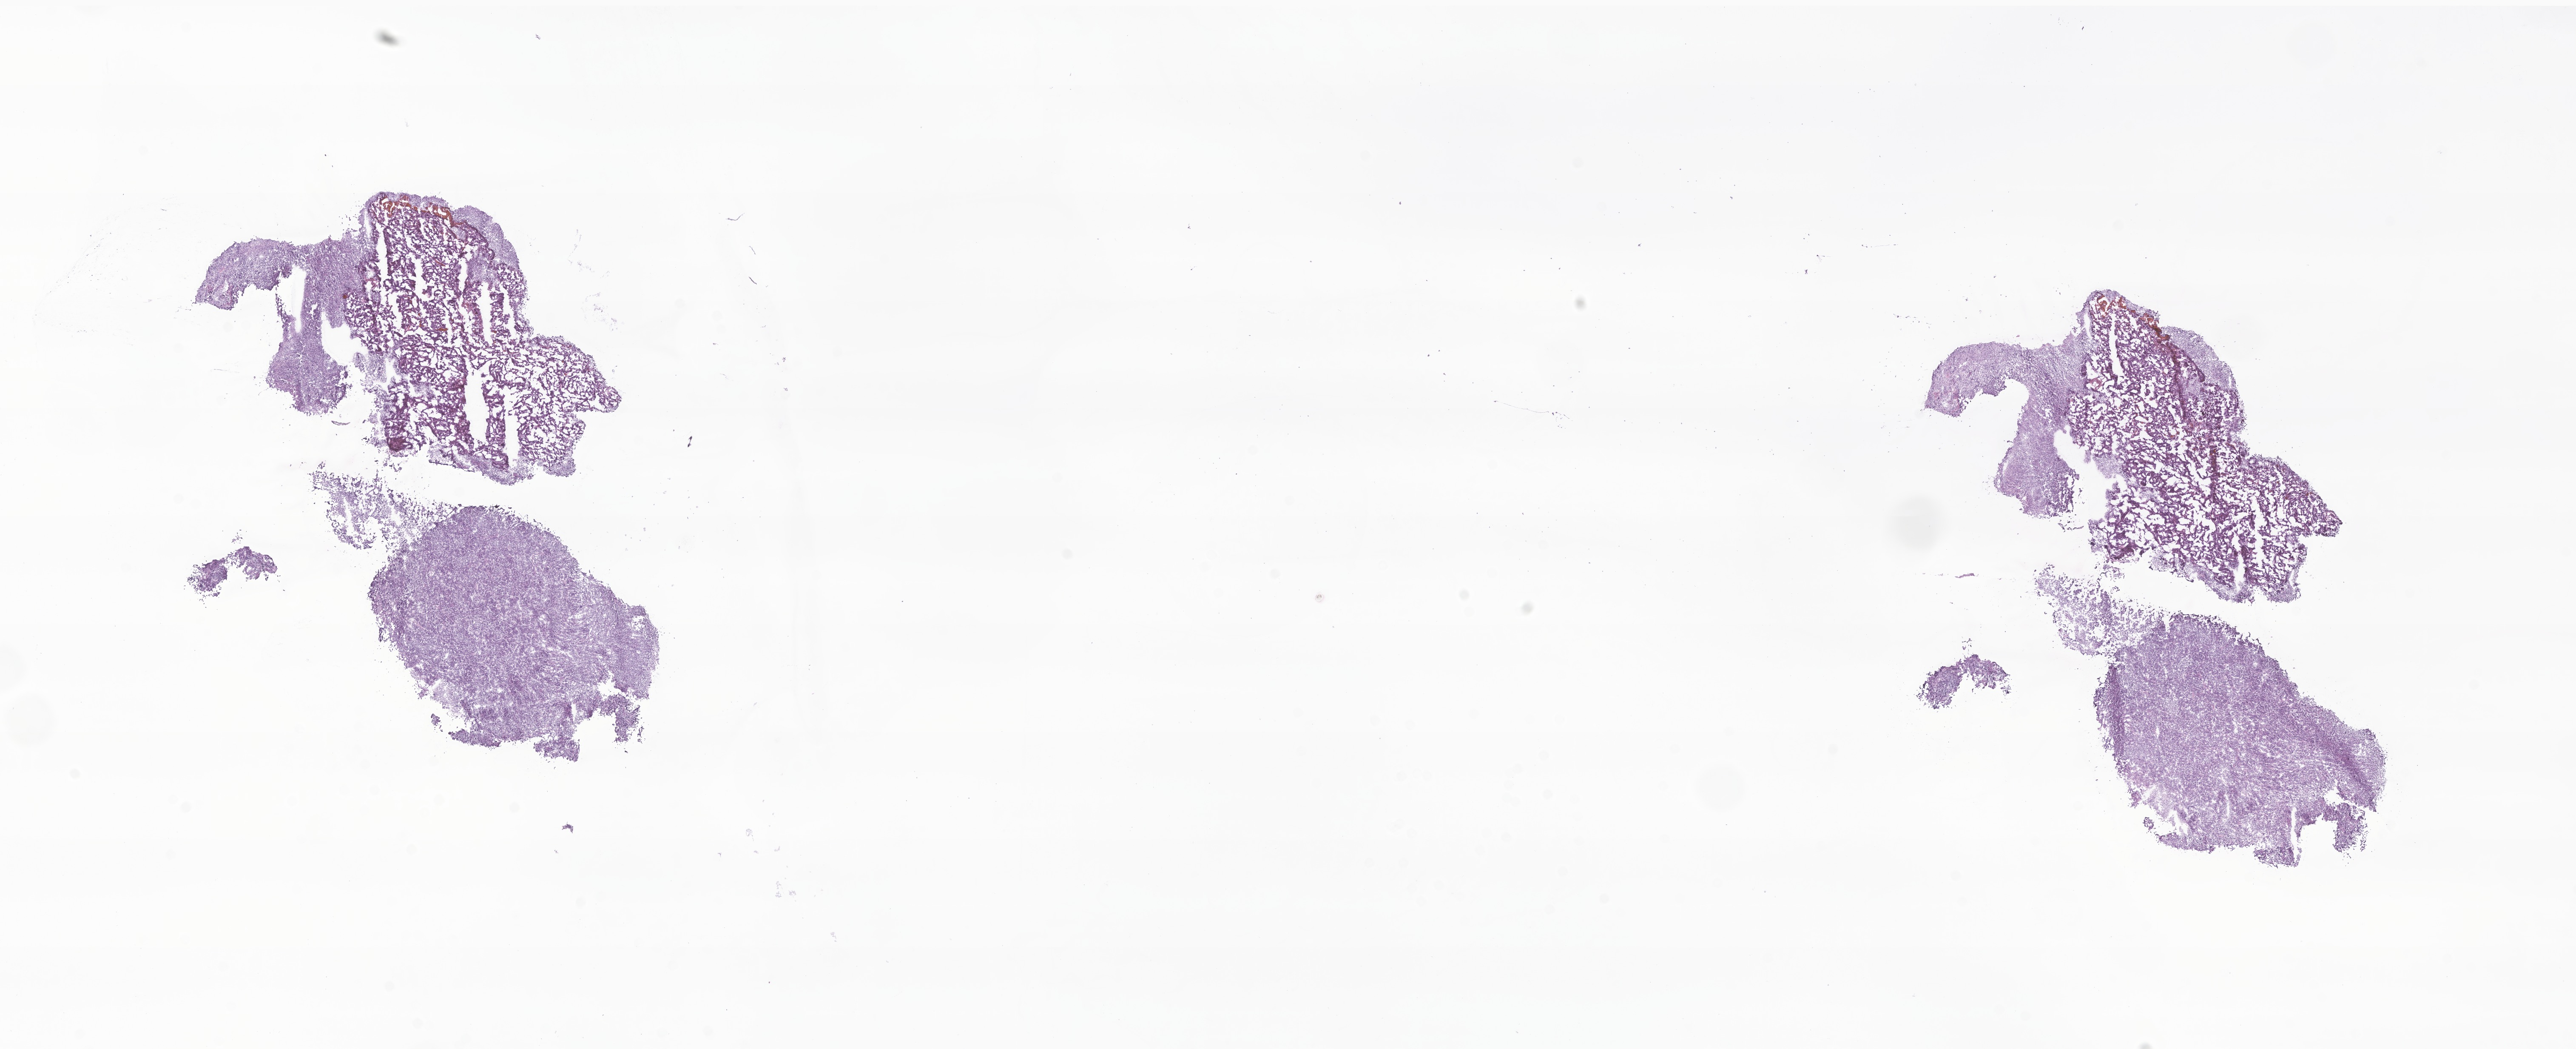
H&E whole-slide image of tumor tissue from the cerebellum, low-resolution overview of the scanned area, about 25.5 x 10.4 mm, frozen section (OCT-embedded). Patient: male, age 136 months.
- diagnosis (ICD-O-3 morphology term): Medulloblastoma, NOS